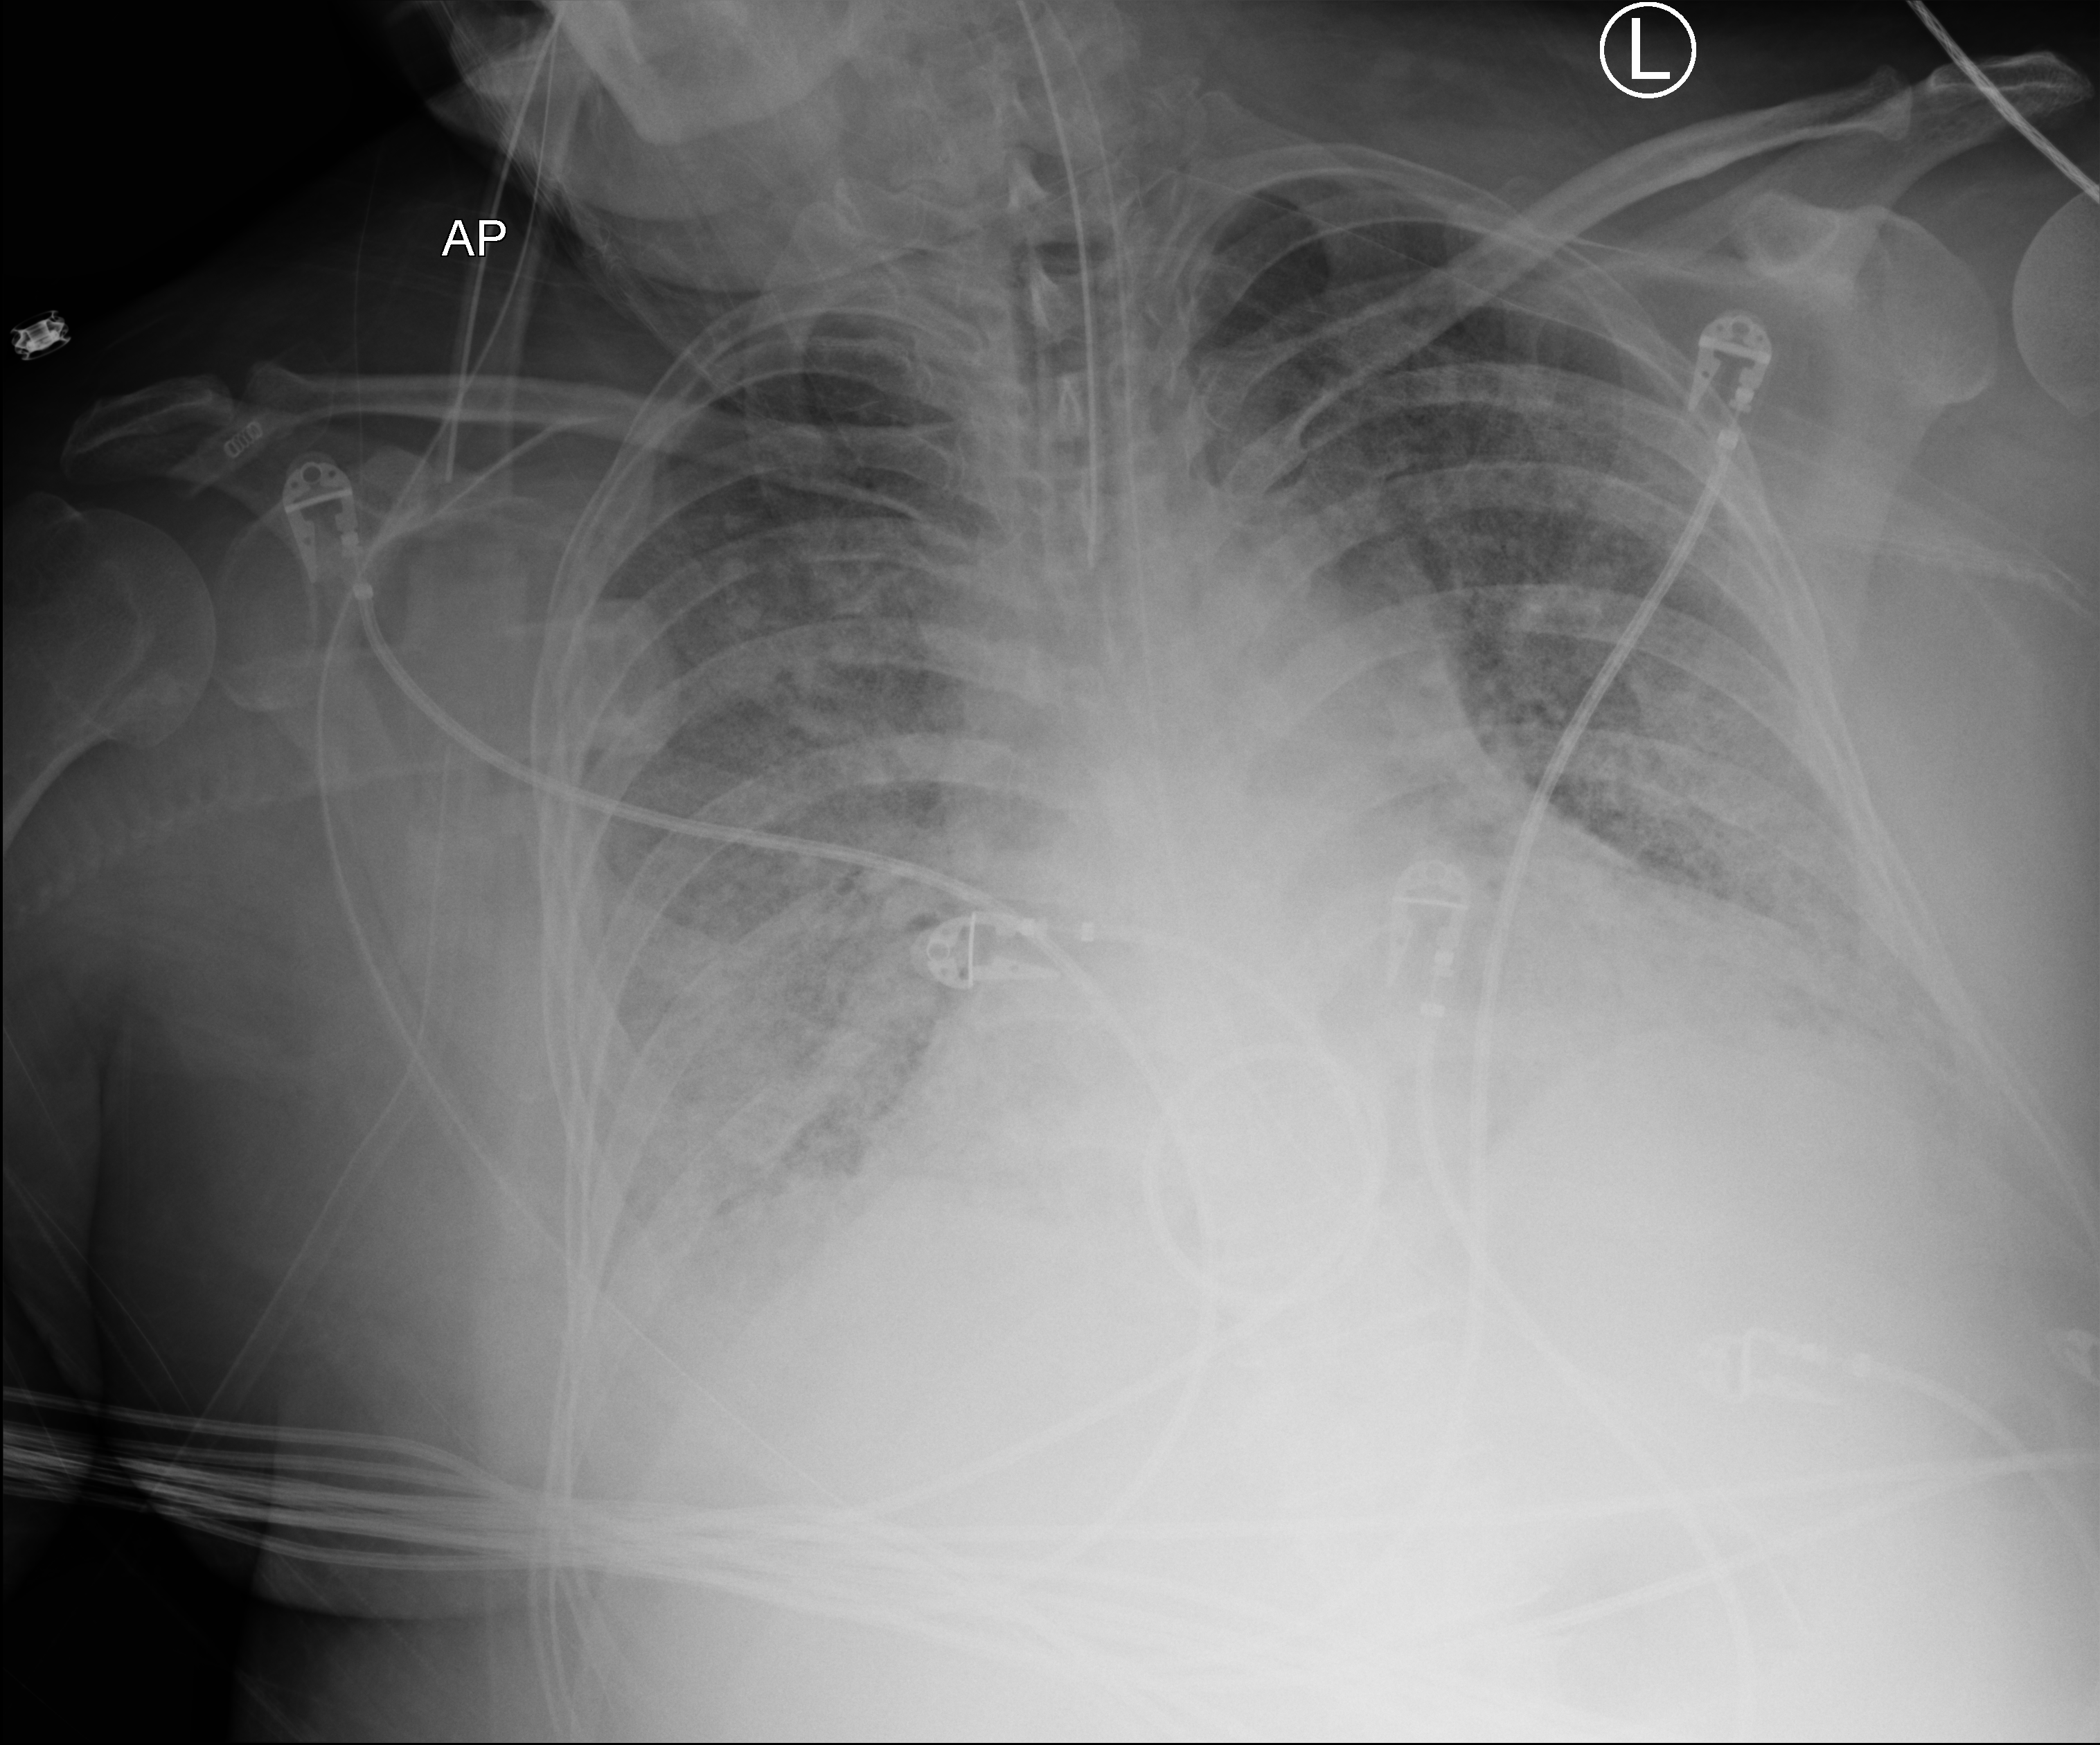
Chest X-ray (portable); anteroposterior (AP) projection. Adult patient hospitalised with COVID-19, age 18–59 years.
From the hospital-stay record, not from the radiograph (when in the stay this image was taken is not recorded): diabetes (admission record): no; mechanically ventilated during this hospital stay: yes; chronic kidney disease (admission record): no.